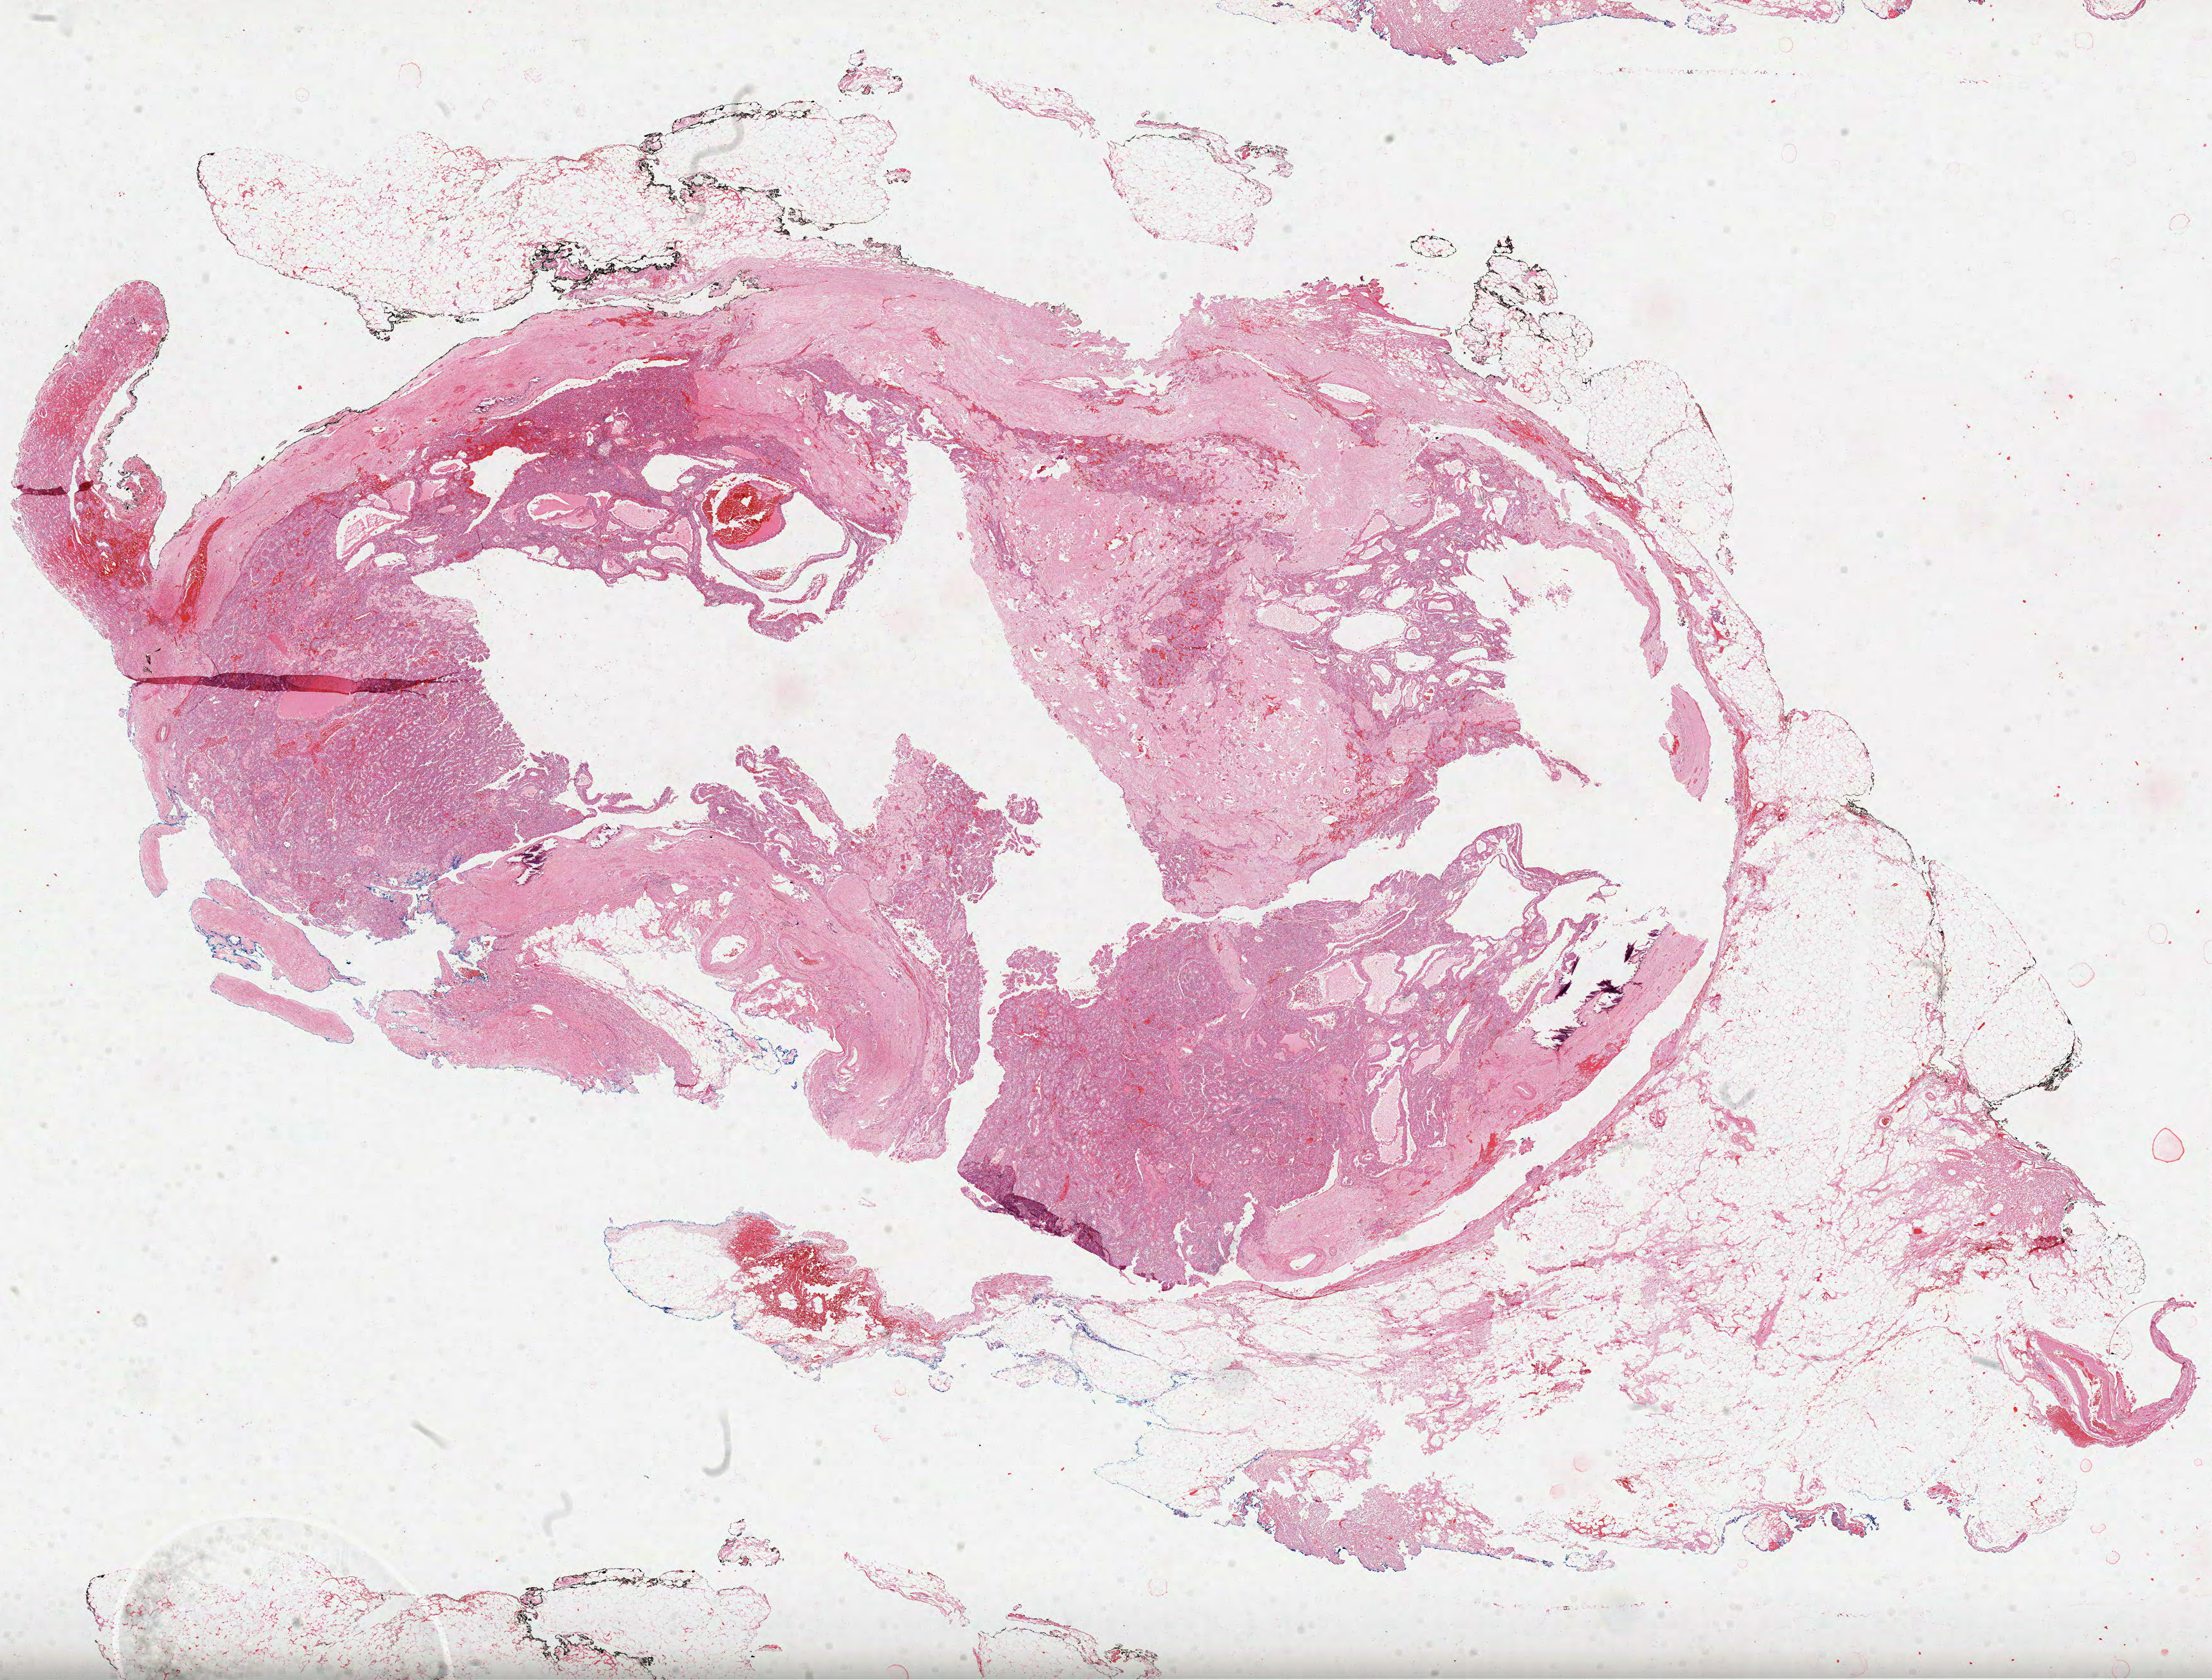
Whole-slide histology image, H&E, shown as a low-resolution overview of the whole scanned area (about 28.0 x 21.3 mm, slide scanned at 40x); formalin-fixed paraffin-embedded (FFPE) diagnostic section; kidney, primary tumour sample. Male, age 58 years at initial diagnosis.
Diagnosis: Papillary adenocarcinoma, NOS. TNM: T1a NX MX. AJCC pathologic stage: I (6th edition).